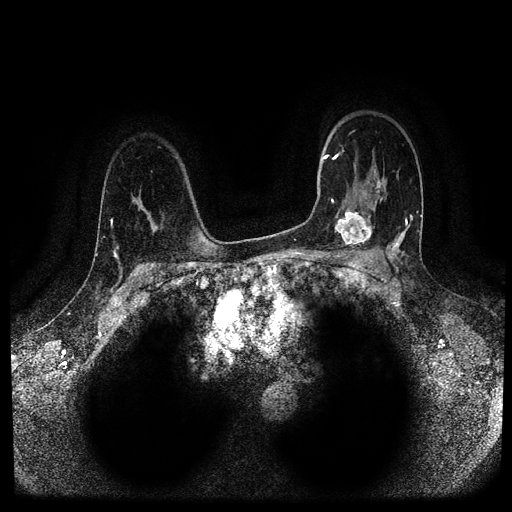
Breast MRI (dynamic contrast-enhanced, multi-phase), one axial slice; position 72 of 116 along the scan axis; dynamic contrast-enhanced series, time point 2 of 5 at this slice position (early post-contrast); 1.5 T; TE 2.6 ms, TR 5.3 ms; 2 mm slice thickness; 512 × 512 image matrix, field of view 350 × 350 mm. Patient: female, 44 years.
Structures marked on this image (semi-automatic segmentation, software-assisted and operator-edited):
- breast lesion (labelled 'tumour' in the annotation; benign lesions carry a separate 'benign' label): box from (x=334, y=208) to (x=376, y=252) px